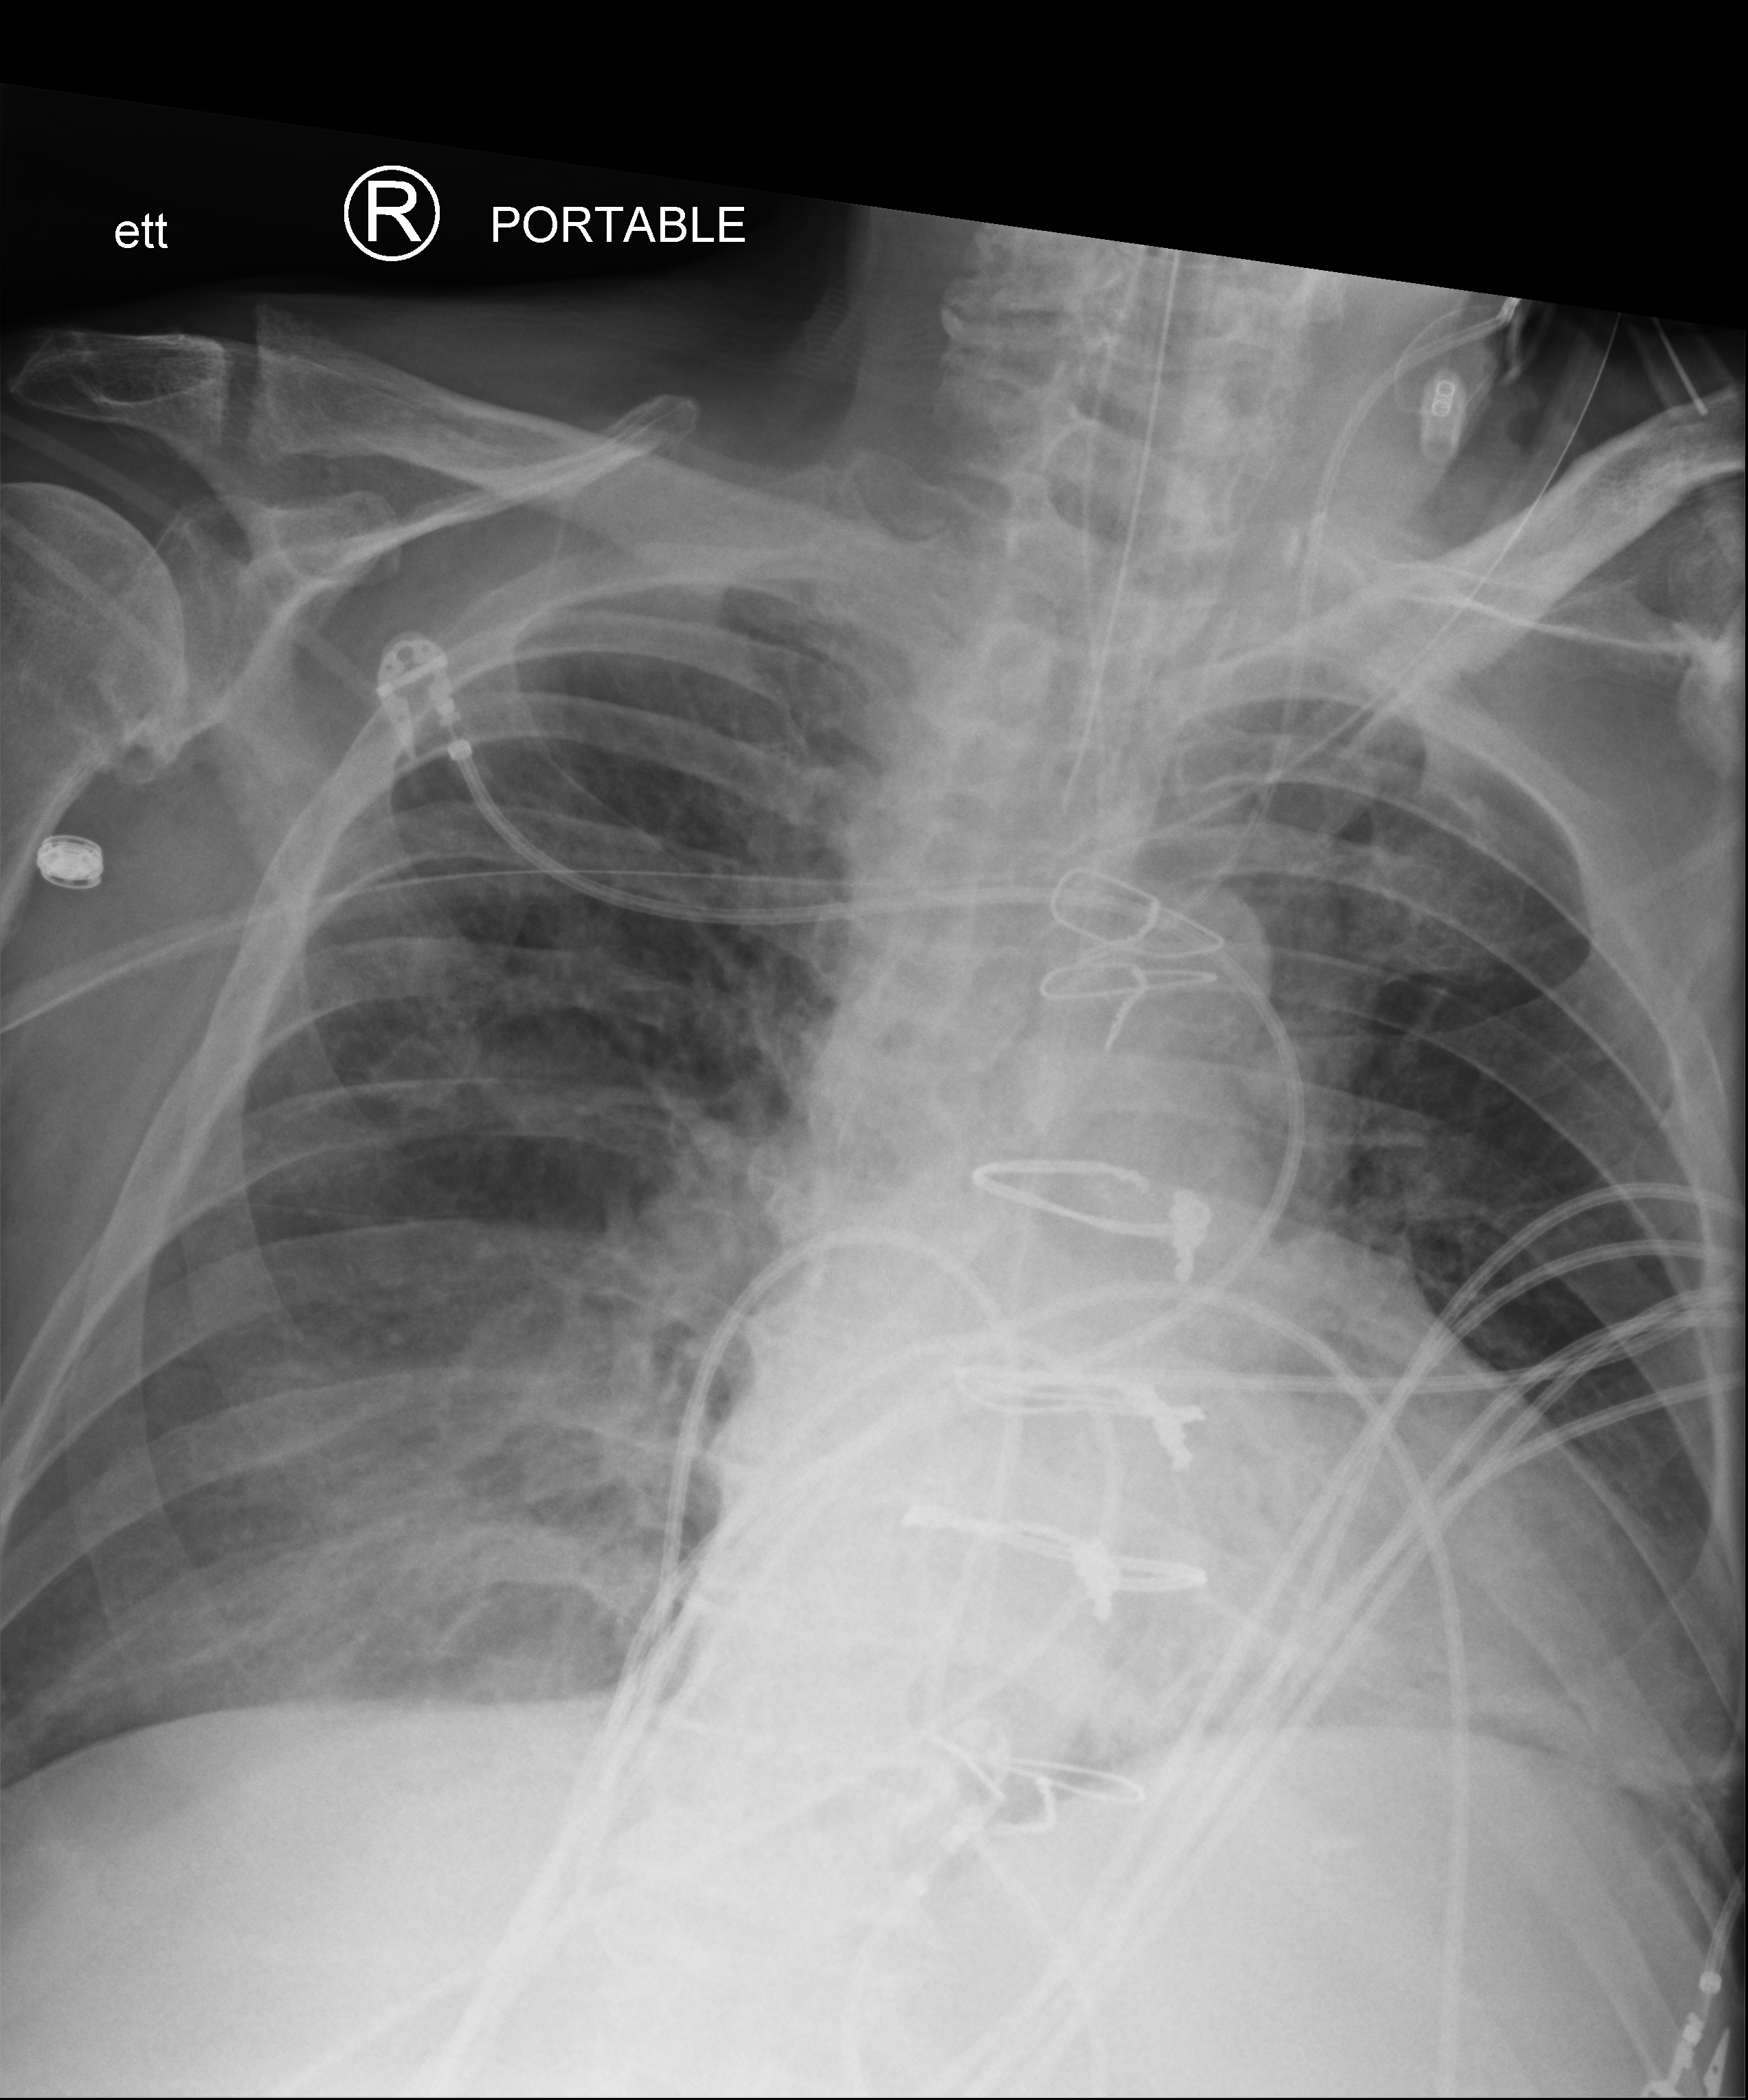
Bedside chest radiograph (computed radiography). Male patient hospitalised with COVID-19, age 60–74 years.
Hospital-stay facts (about this admission, not read from this image; timing relative to this image not recorded): COPD (admission record): no; length of hospital stay: 16 days; mechanically ventilated during this hospital stay: yes.